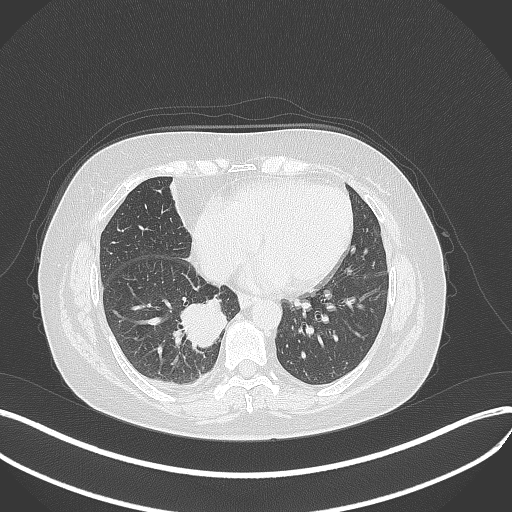
Chest CT, one axial slice. Position 131 of 381 along the scan axis. 120 kVp. Lung window (W 1500 / L -600 HU). 1 mm slice thickness. 512 × 512 image matrix, field of view 400 × 400 mm. Patient: female, 56 years. From the clinical record (not read from this slice): clinical TNM (as recorded): T2b N1 M0; histopathological grade: G3.
Annotated regions visible in this slice (rectangle marked by the reading radiologist):
- lung tumour (recorded histology: small cell carcinoma): box from (x=178, y=296) to (x=226, y=355) px